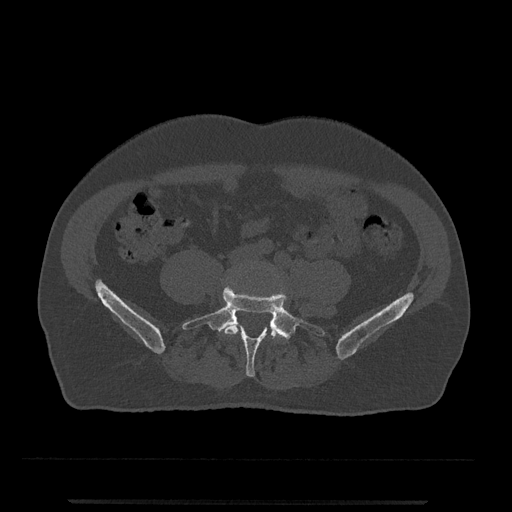
CT including the spine, one axial slice; slice 88 of 797 in the series (ordered by position); reconstruction kernel Br40s/3; 120 kVp; bone window (W 1800 / L 400 HU); 0.5 mm slice thickness; 512 × 512 image matrix, field of view 419 × 419 mm. Male patient, age 63 years. Case-level facts recorded for this patient, not image findings: primary cancer: prostate.
Outlined on this slice (semi-automatic segmentation, software-assisted and operator-edited):
- L4 vertebra: bounding box <223,320,280,340> (left, top, right, bottom; pixels)
- L5 vertebra: <182,286,325,377>